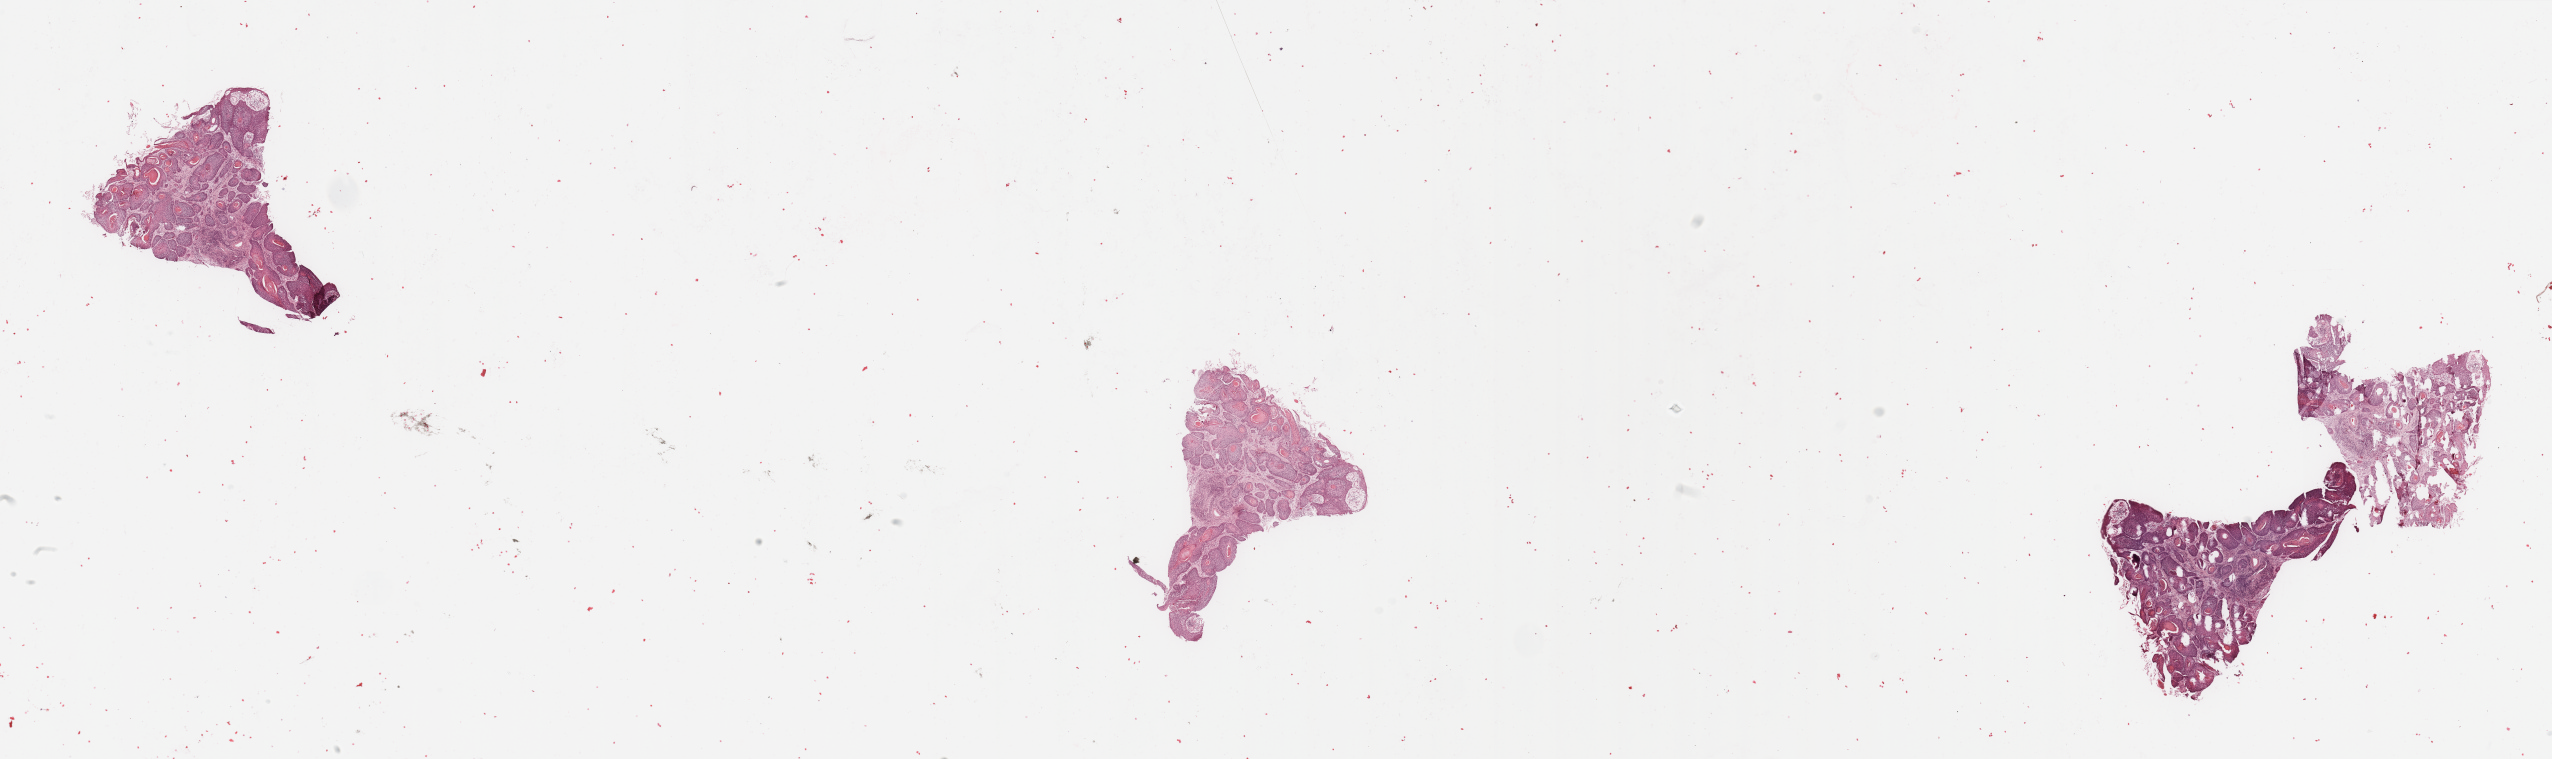
Whole-slide histology image, H&E, shown as a low-resolution overview of the whole scanned area (about 40.4 x 12.0 mm, from a 20x scan); tumour tissue sample, sampled site: floor of mouth. Patient: female, age 50 years. Histologic grade: G1 (well differentiated). Pathologist review of this section (percent, as recorded): tumour nuclei 85%, necrosis 5%.
• primary tumour site (as recorded): oral cavity
• AJCC pathologic stage: IVA
• diagnosis: Squamous cell carcinoma, NOS (floor of mouth, NOS)